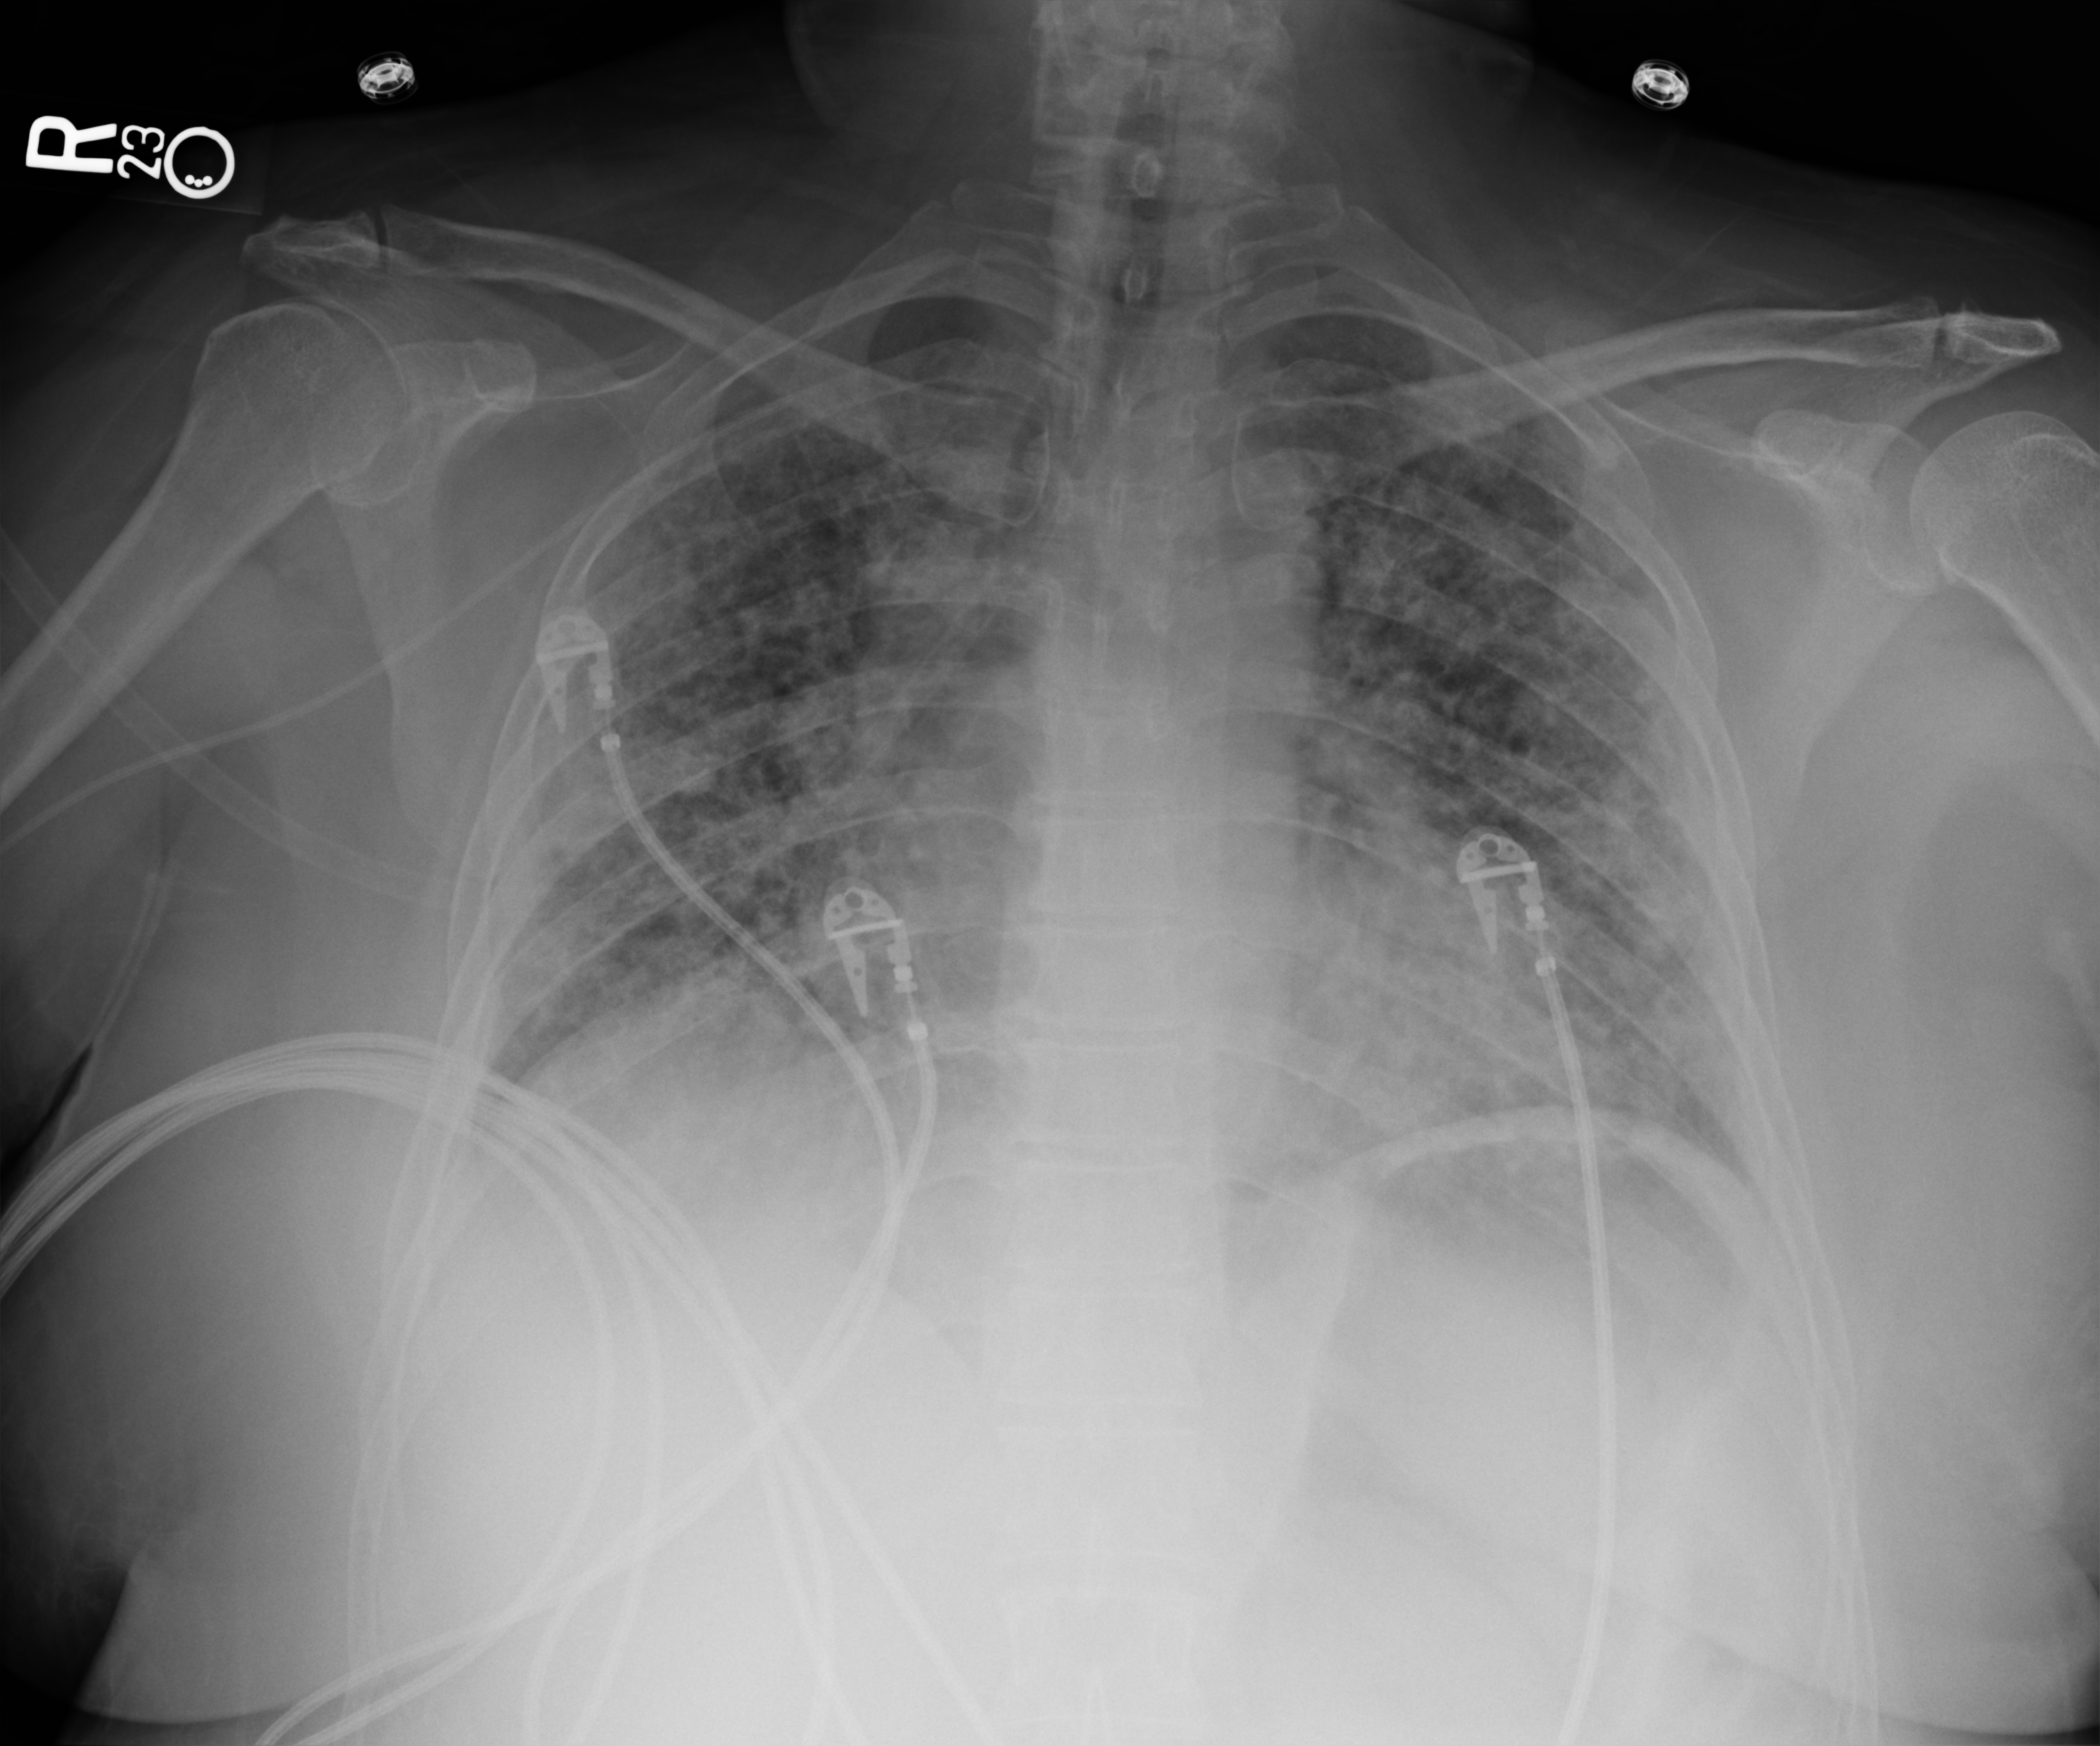
Chest X-ray (portable). Patient hospitalised with COVID-19; female, aged 18–59 years.
From the hospital-stay record, not from the radiograph (when in the stay this image was taken is not recorded):
- length of hospital stay: 21 days
- mechanically ventilated during this hospital stay: no